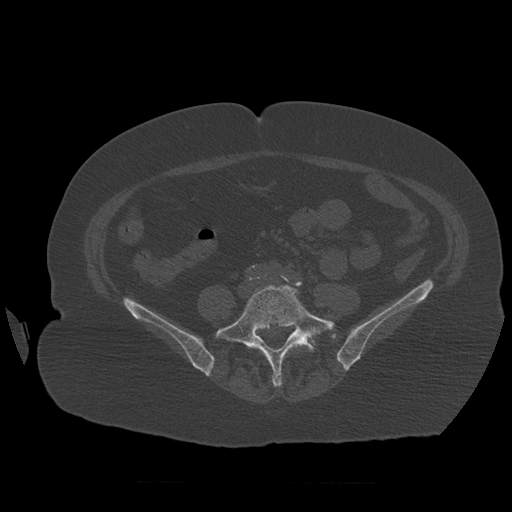
CT including the spine, one axial slice. Reconstruction kernel STANDARD. Bone window (W 1800 / L 400 HU). 1.25 mm slice thickness. 512 × 512 image matrix. Patient age 81 years. From the clinical record (not read from this slice): primary cancer: renal; vertebrae with lytic lesions (as recorded): L1.
Annotated regions visible in this slice (semi-automatically segmented with operator editing):
- L5 vertebra: box from (x=216, y=284) to (x=335, y=387) px